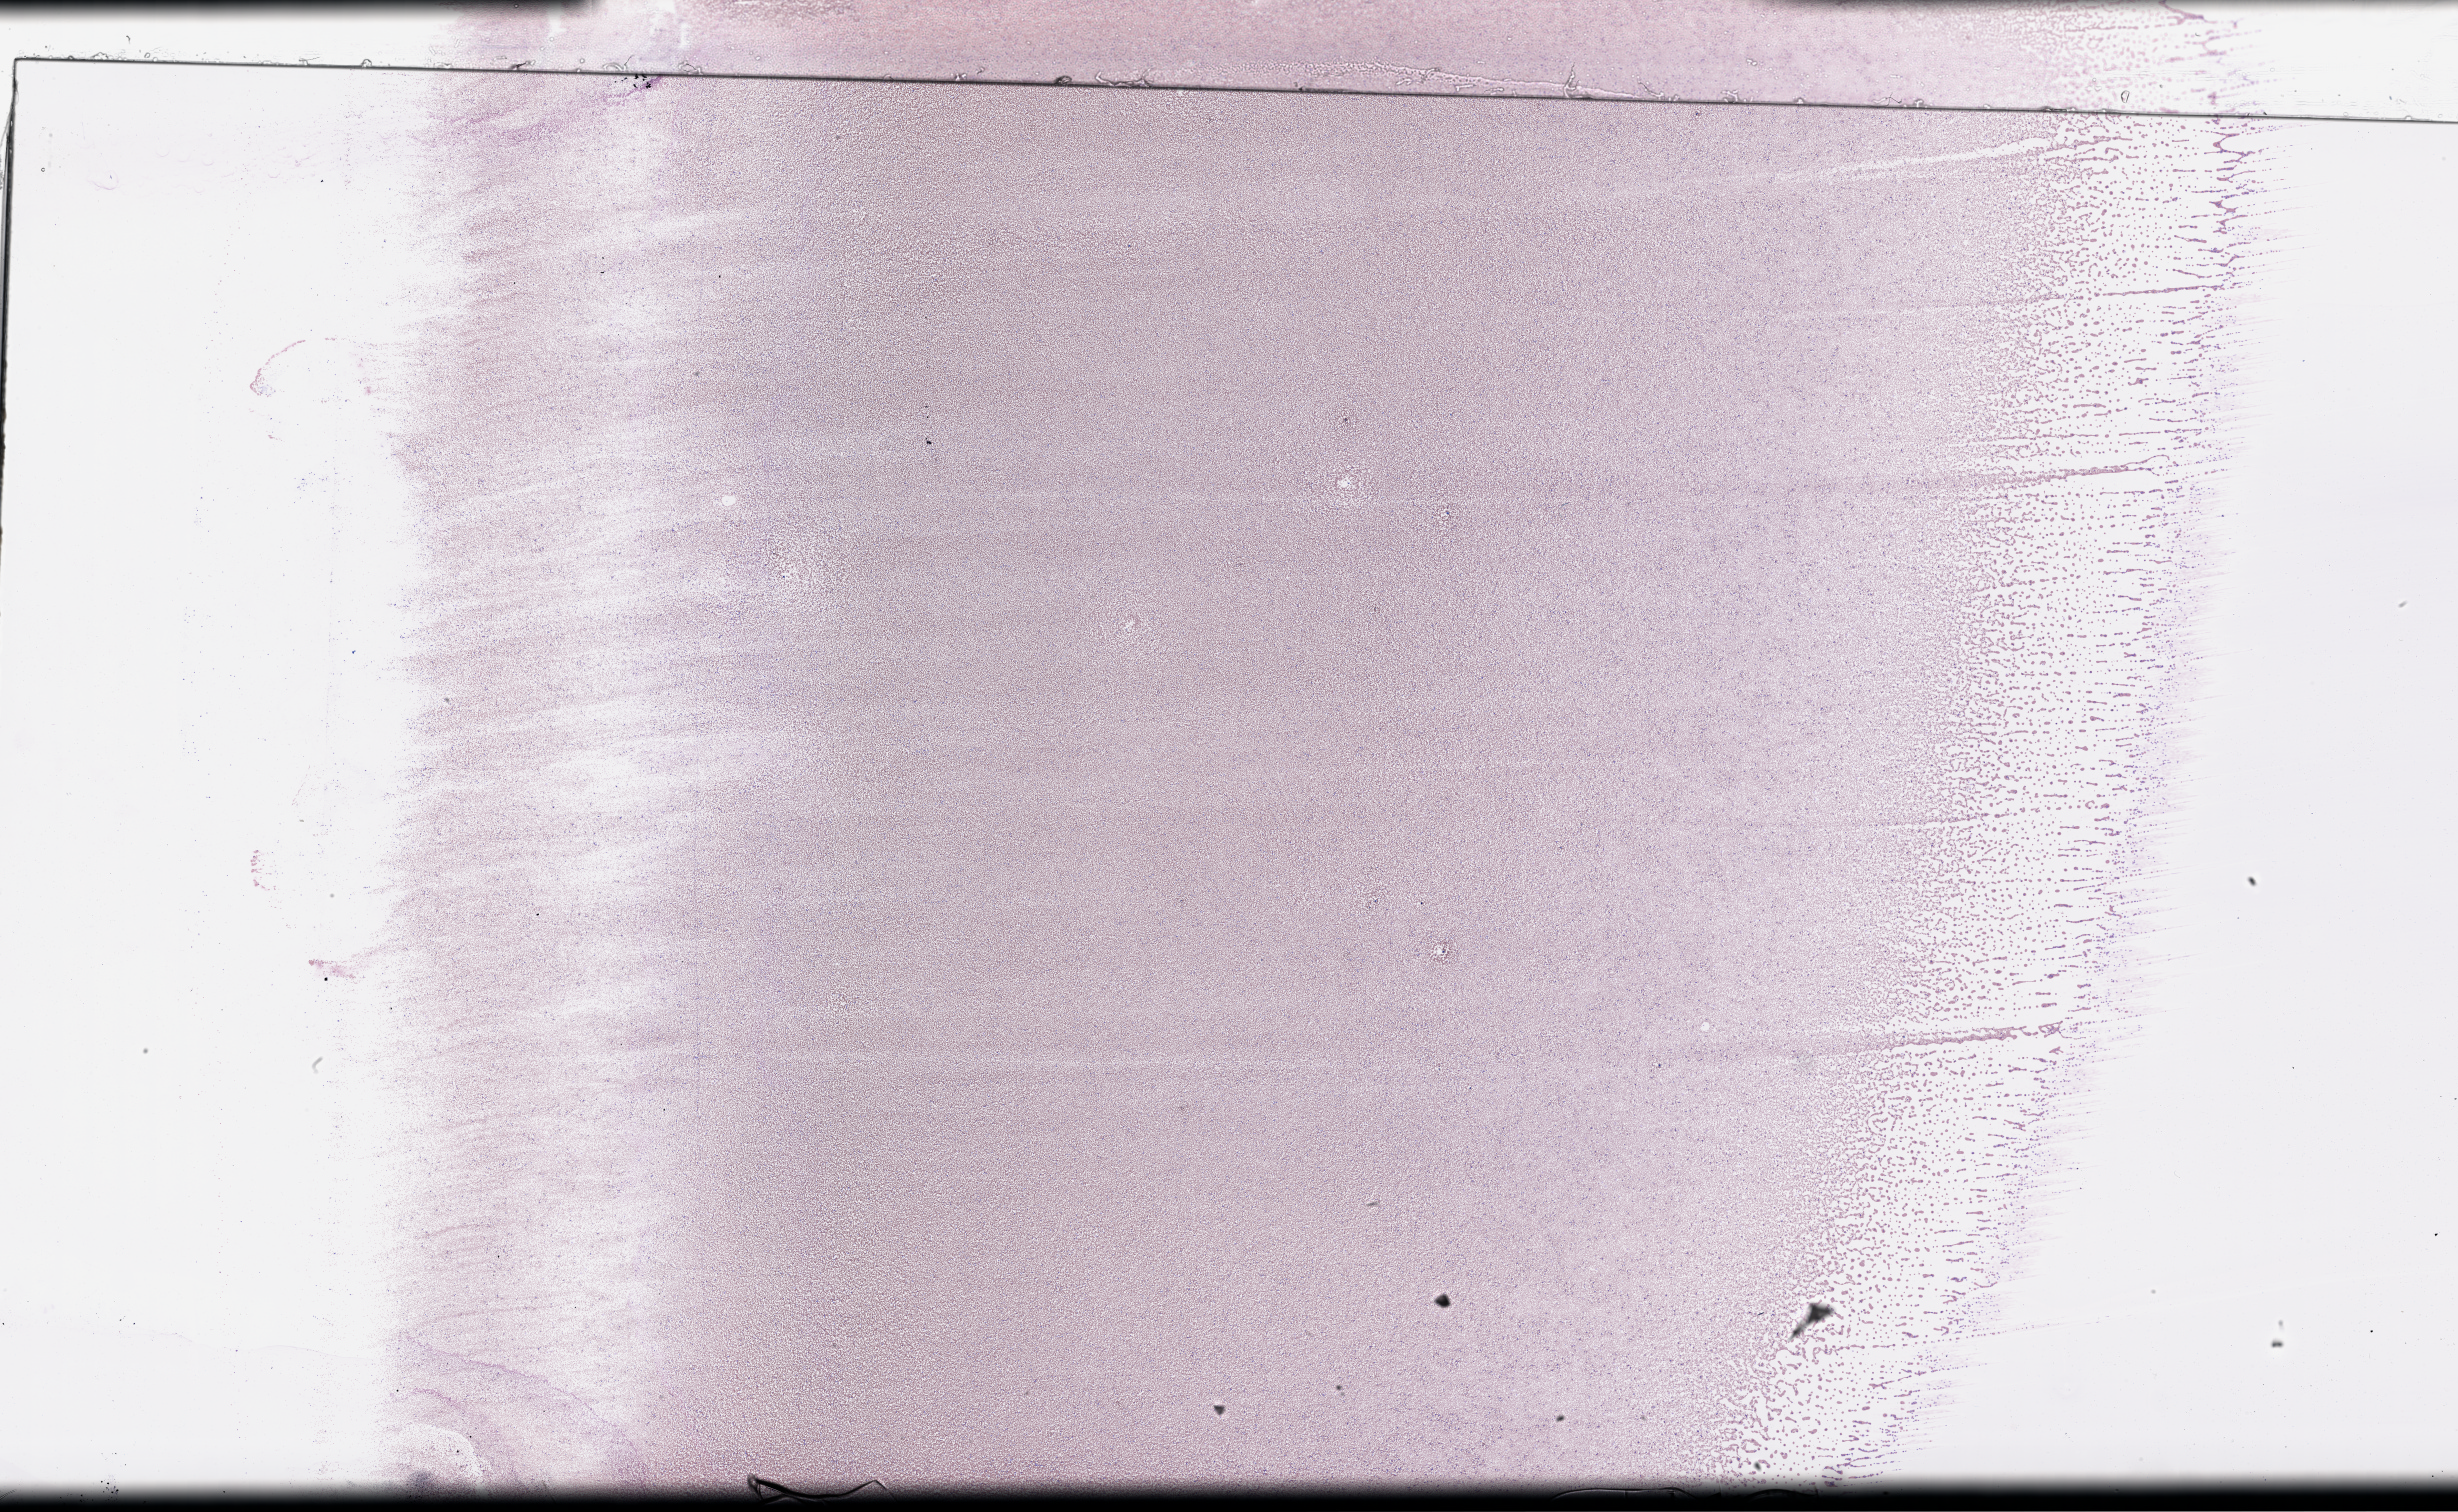
Digitized Hematoxylin and eosin (H&E) stained tissue section (whole slide) — shown as a low-resolution overview of the whole scanned area (about 39.7 x 24.4 mm, slide scanned at 40x). Peripheral blood (leukaemic) sample. Male, 67 y/o.
FAB classification: M2. Diagnosis: Acute Myeloid Leukemia. WHO classification: AML with maturation.